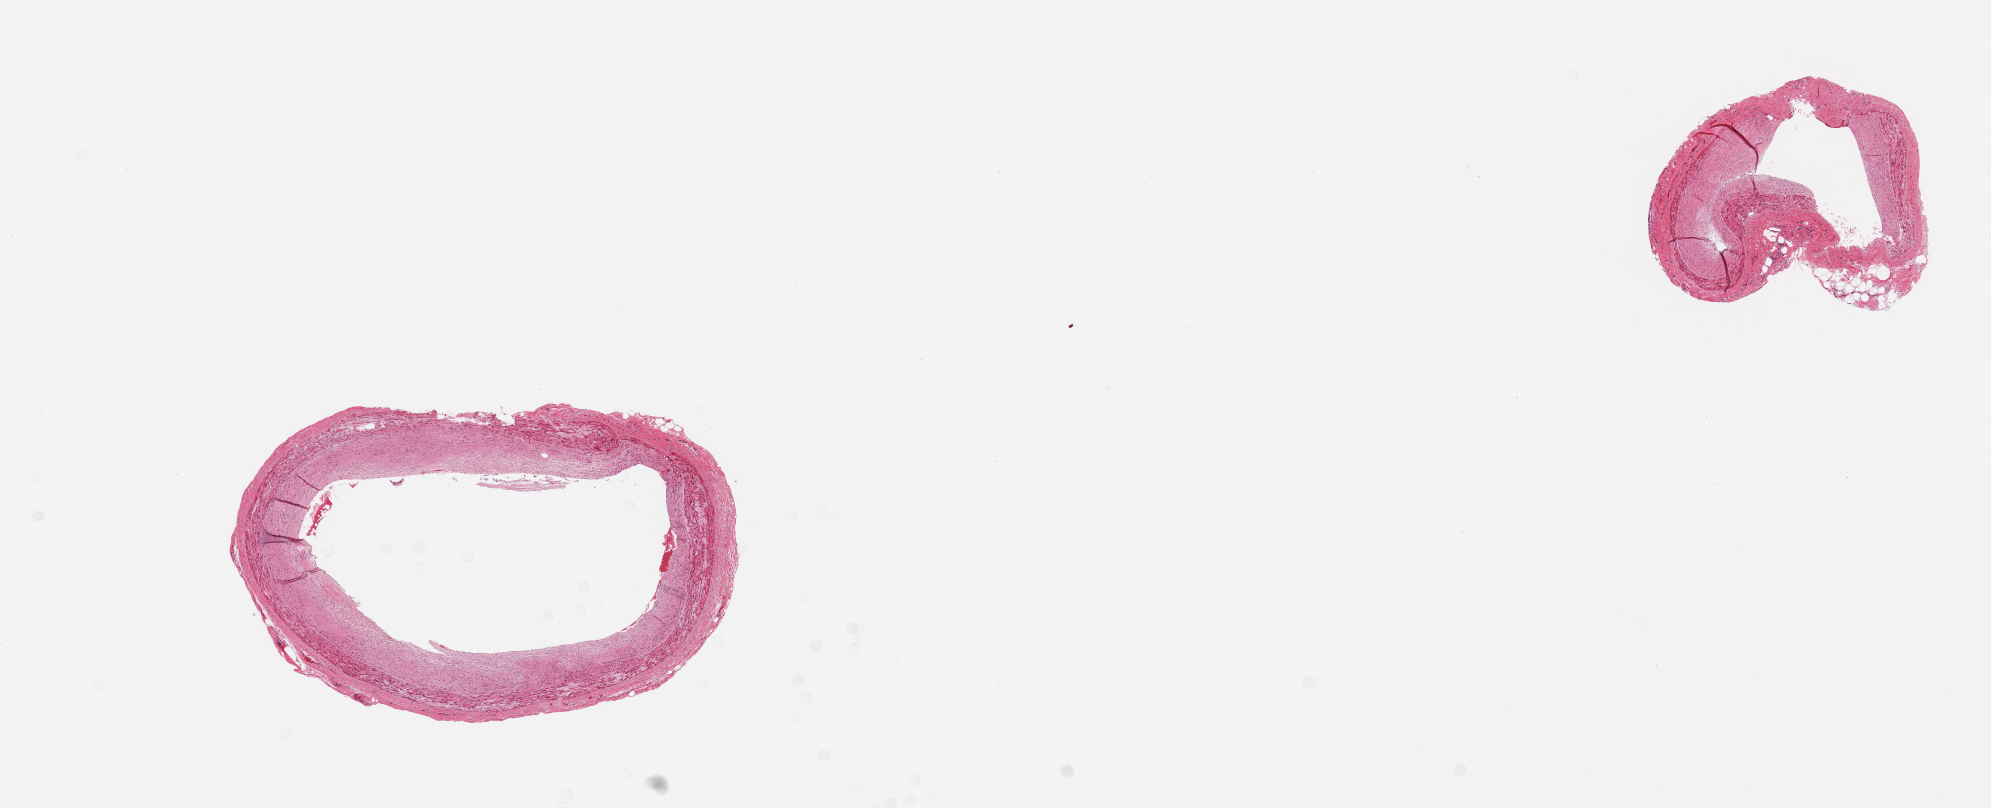
Digitized haematoxylin and eosin-stained section, whole scanned area (about 15.8 x 6.4 mm) shown as a low-resolution overview. PAXgene-fixed paraffin-embedded (PFPE) section. Target tissue: coronary artery. Tissue donor sample. Donor sex: male.
Pathologist's review note for this sample: 2 pieces; atherosclerosis.